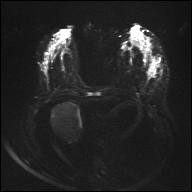
Breast MRI, one axial slice. Slice 14 of 32 in the series (ordered by position). Diffusion-weighted series; image 2 of 4 stored at this slice position (different b-values; order by instance number). 1.5 T. 4 mm slice thickness. 192 × 192 image matrix, field of view 360 × 360 mm. Female patient.
Structures marked on this image (manually delineated by an expert):
- tumour on diffusion-weighted imaging: bounding box (x1, y1, x2, y2) in pixels: (148, 71, 155, 75)